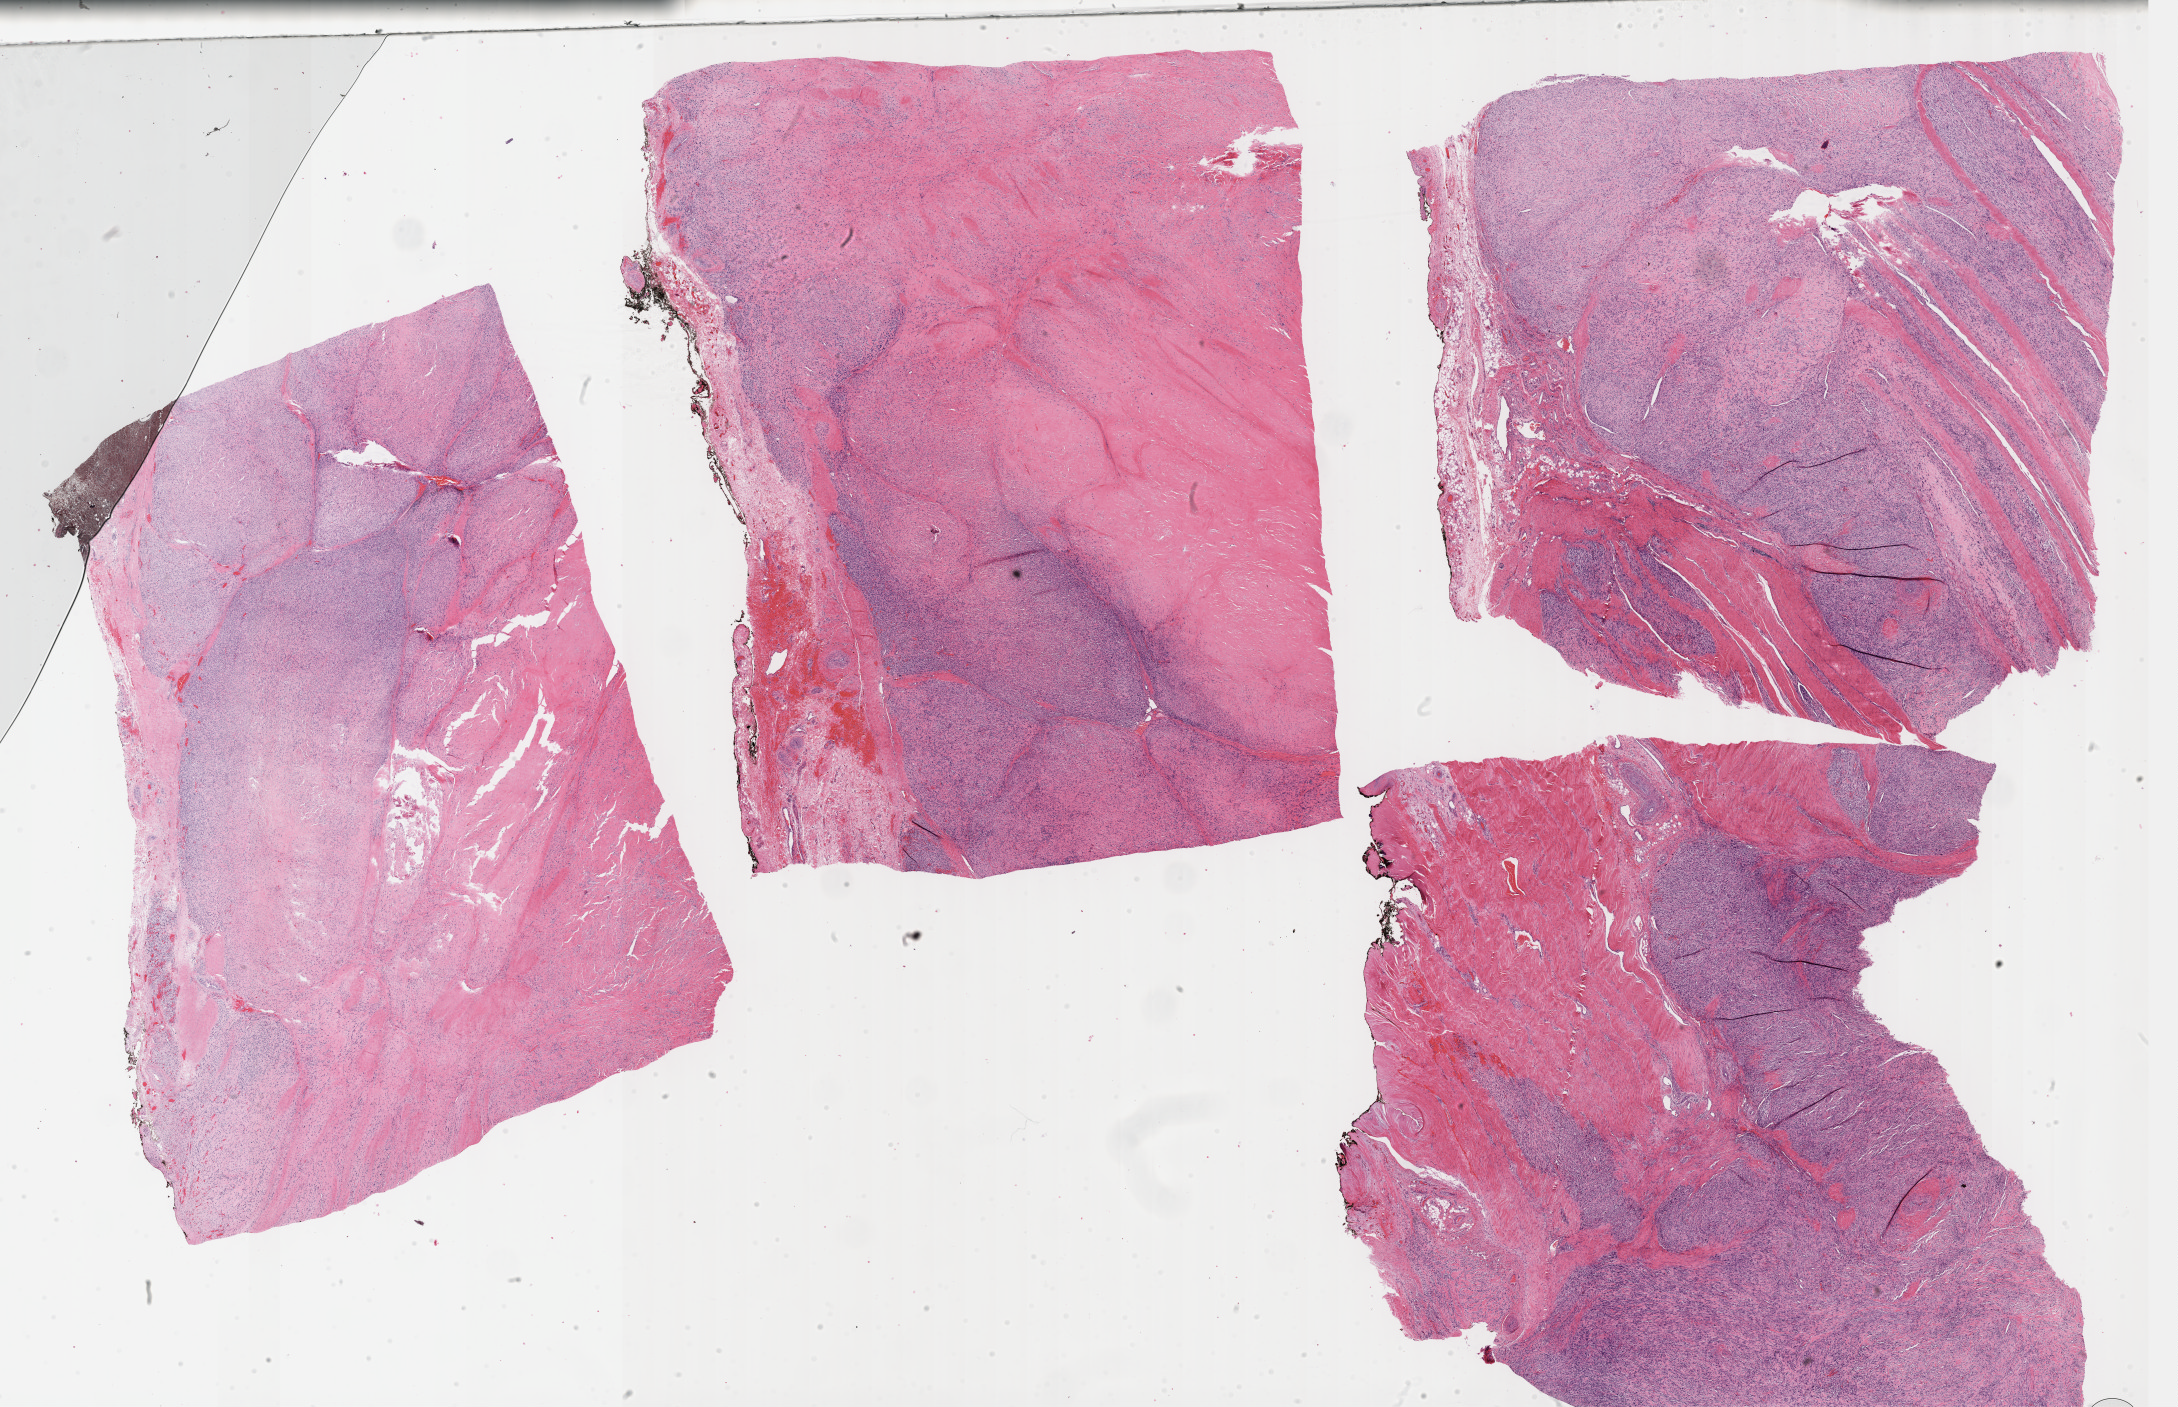
Whole-slide histology image, Hematoxylin and eosin (H&E) stained, whole scanned area (about 35.2 x 22.7 mm) shown as a low-resolution overview, formalin-fixed paraffin-embedded (FFPE) diagnostic section, primary tumour sample from the connective, subcutaneous and other soft tissues. Male patient; age at initial diagnosis 74 years.
- histologic diagnosis: Leiomyosarcoma, NOS (connective, subcutaneous and other soft tissues of lower limb and hip)